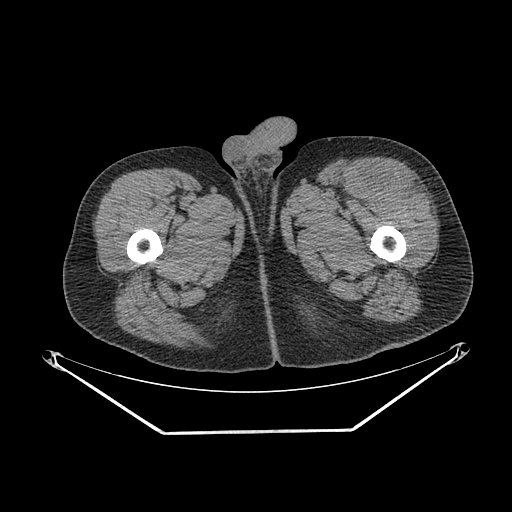
CT of an extremity soft-tissue mass (from a PET/CT study), one axial slice; slice 257 of 267 in the series (ordered by position); reconstruction kernel SOFT; soft-tissue window (W 400 / L 40 HU); 3.75 mm slice thickness; 512 × 512 image matrix, field of view 500 × 500 mm. Male patient. From the clinical record (not read from this slice): histological type: extraskeletal osteosarcoma; grade: high; site of the primary tumour: thigh.
Outlined on this slice (expert contour drawn on MRI and transferred to this co-registered scan by the dataset authors):
- gross tumour volume (mass): bounding box (x1, y1, x2, y2) in pixels: (370, 171, 419, 195)